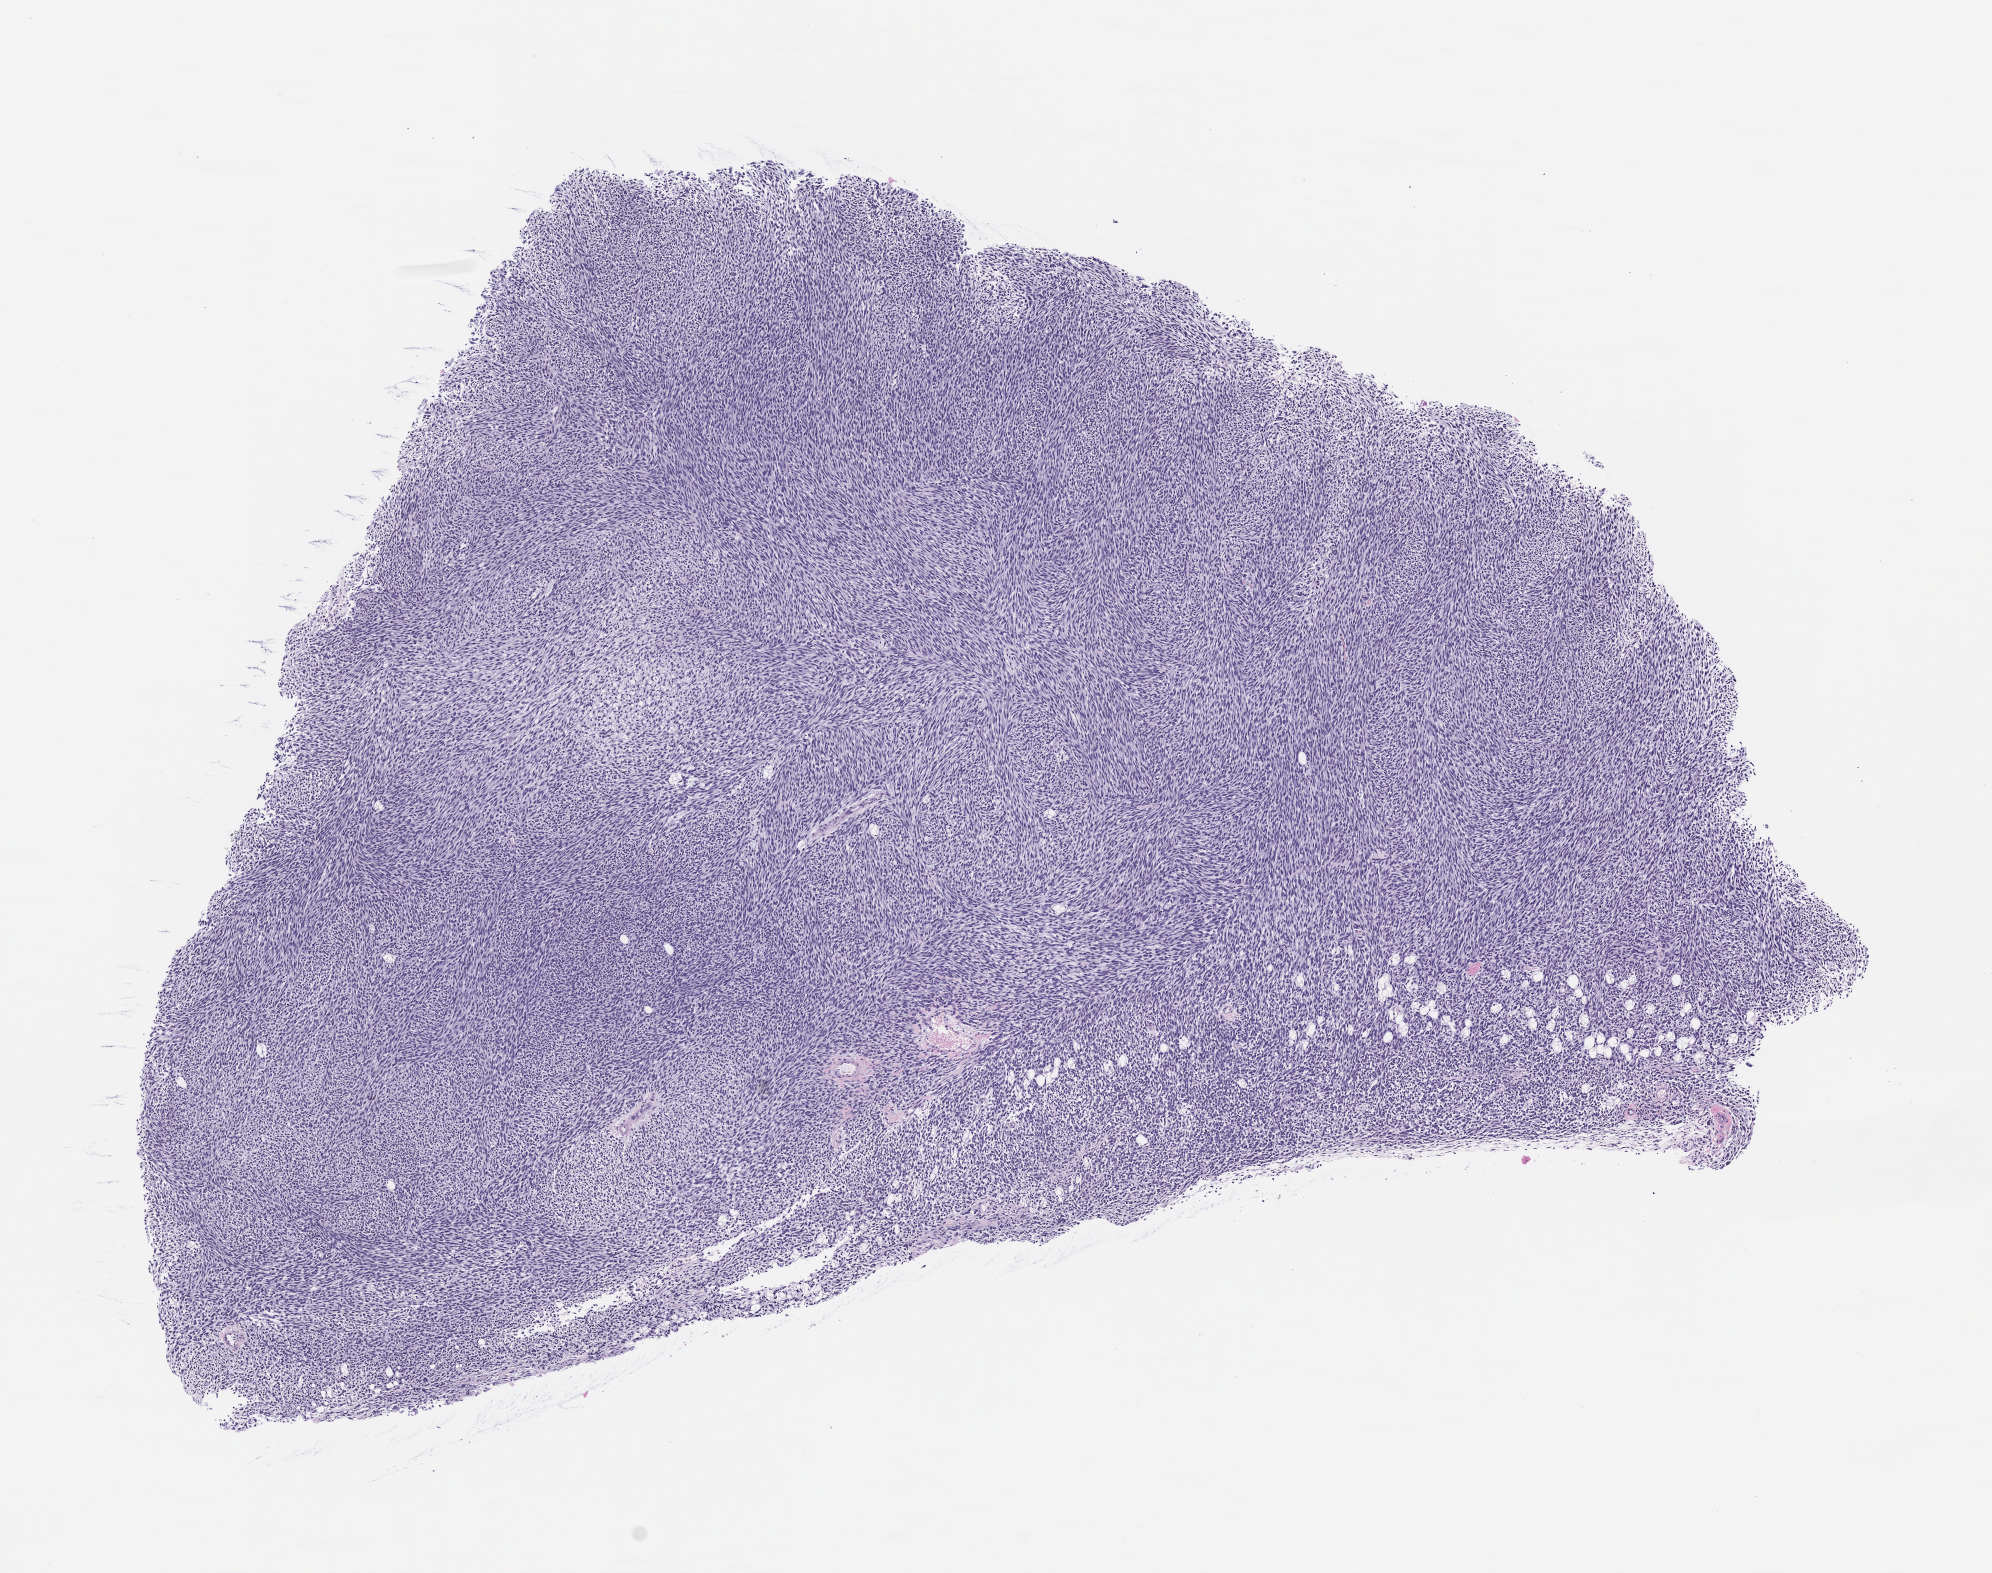
Hematoxylin and eosin (H&E) whole-slide image of a patient-derived xenograft (PDX) tumor grown in a mouse, passage 3 — low-resolution overview of the scanned area, about 8.0 x 6.3 mm; formalin-fixed, paraffin-embedded (FFPE) tissue; tumor site category: musculoskeletal.
Originating patient diagnosis: Synovial Sarcoma.